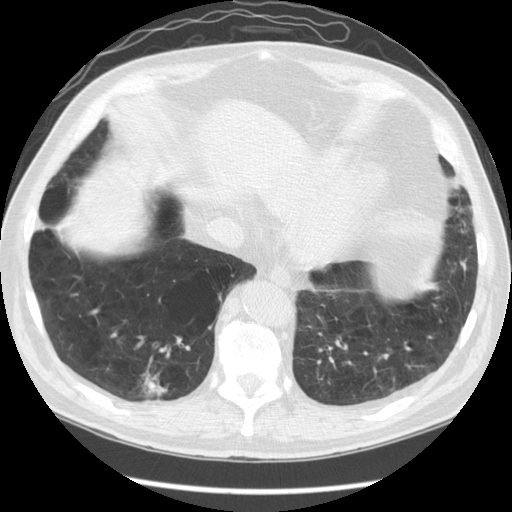
Low-dose screening chest CT, one axial slice; position 40 of 141 along the scan axis; 120 kVp; lung window (W 1500 / L -600 HU); 2.5 mm slice thickness; 512 × 512 image matrix, field of view 370 × 370 mm.
Outlined on this slice (outlined manually by an expert reader):
- lesion 1 (tumor, lower lobe of right lung): bounding box (x1, y1, x2, y2) in pixels: (144, 380, 168, 396)